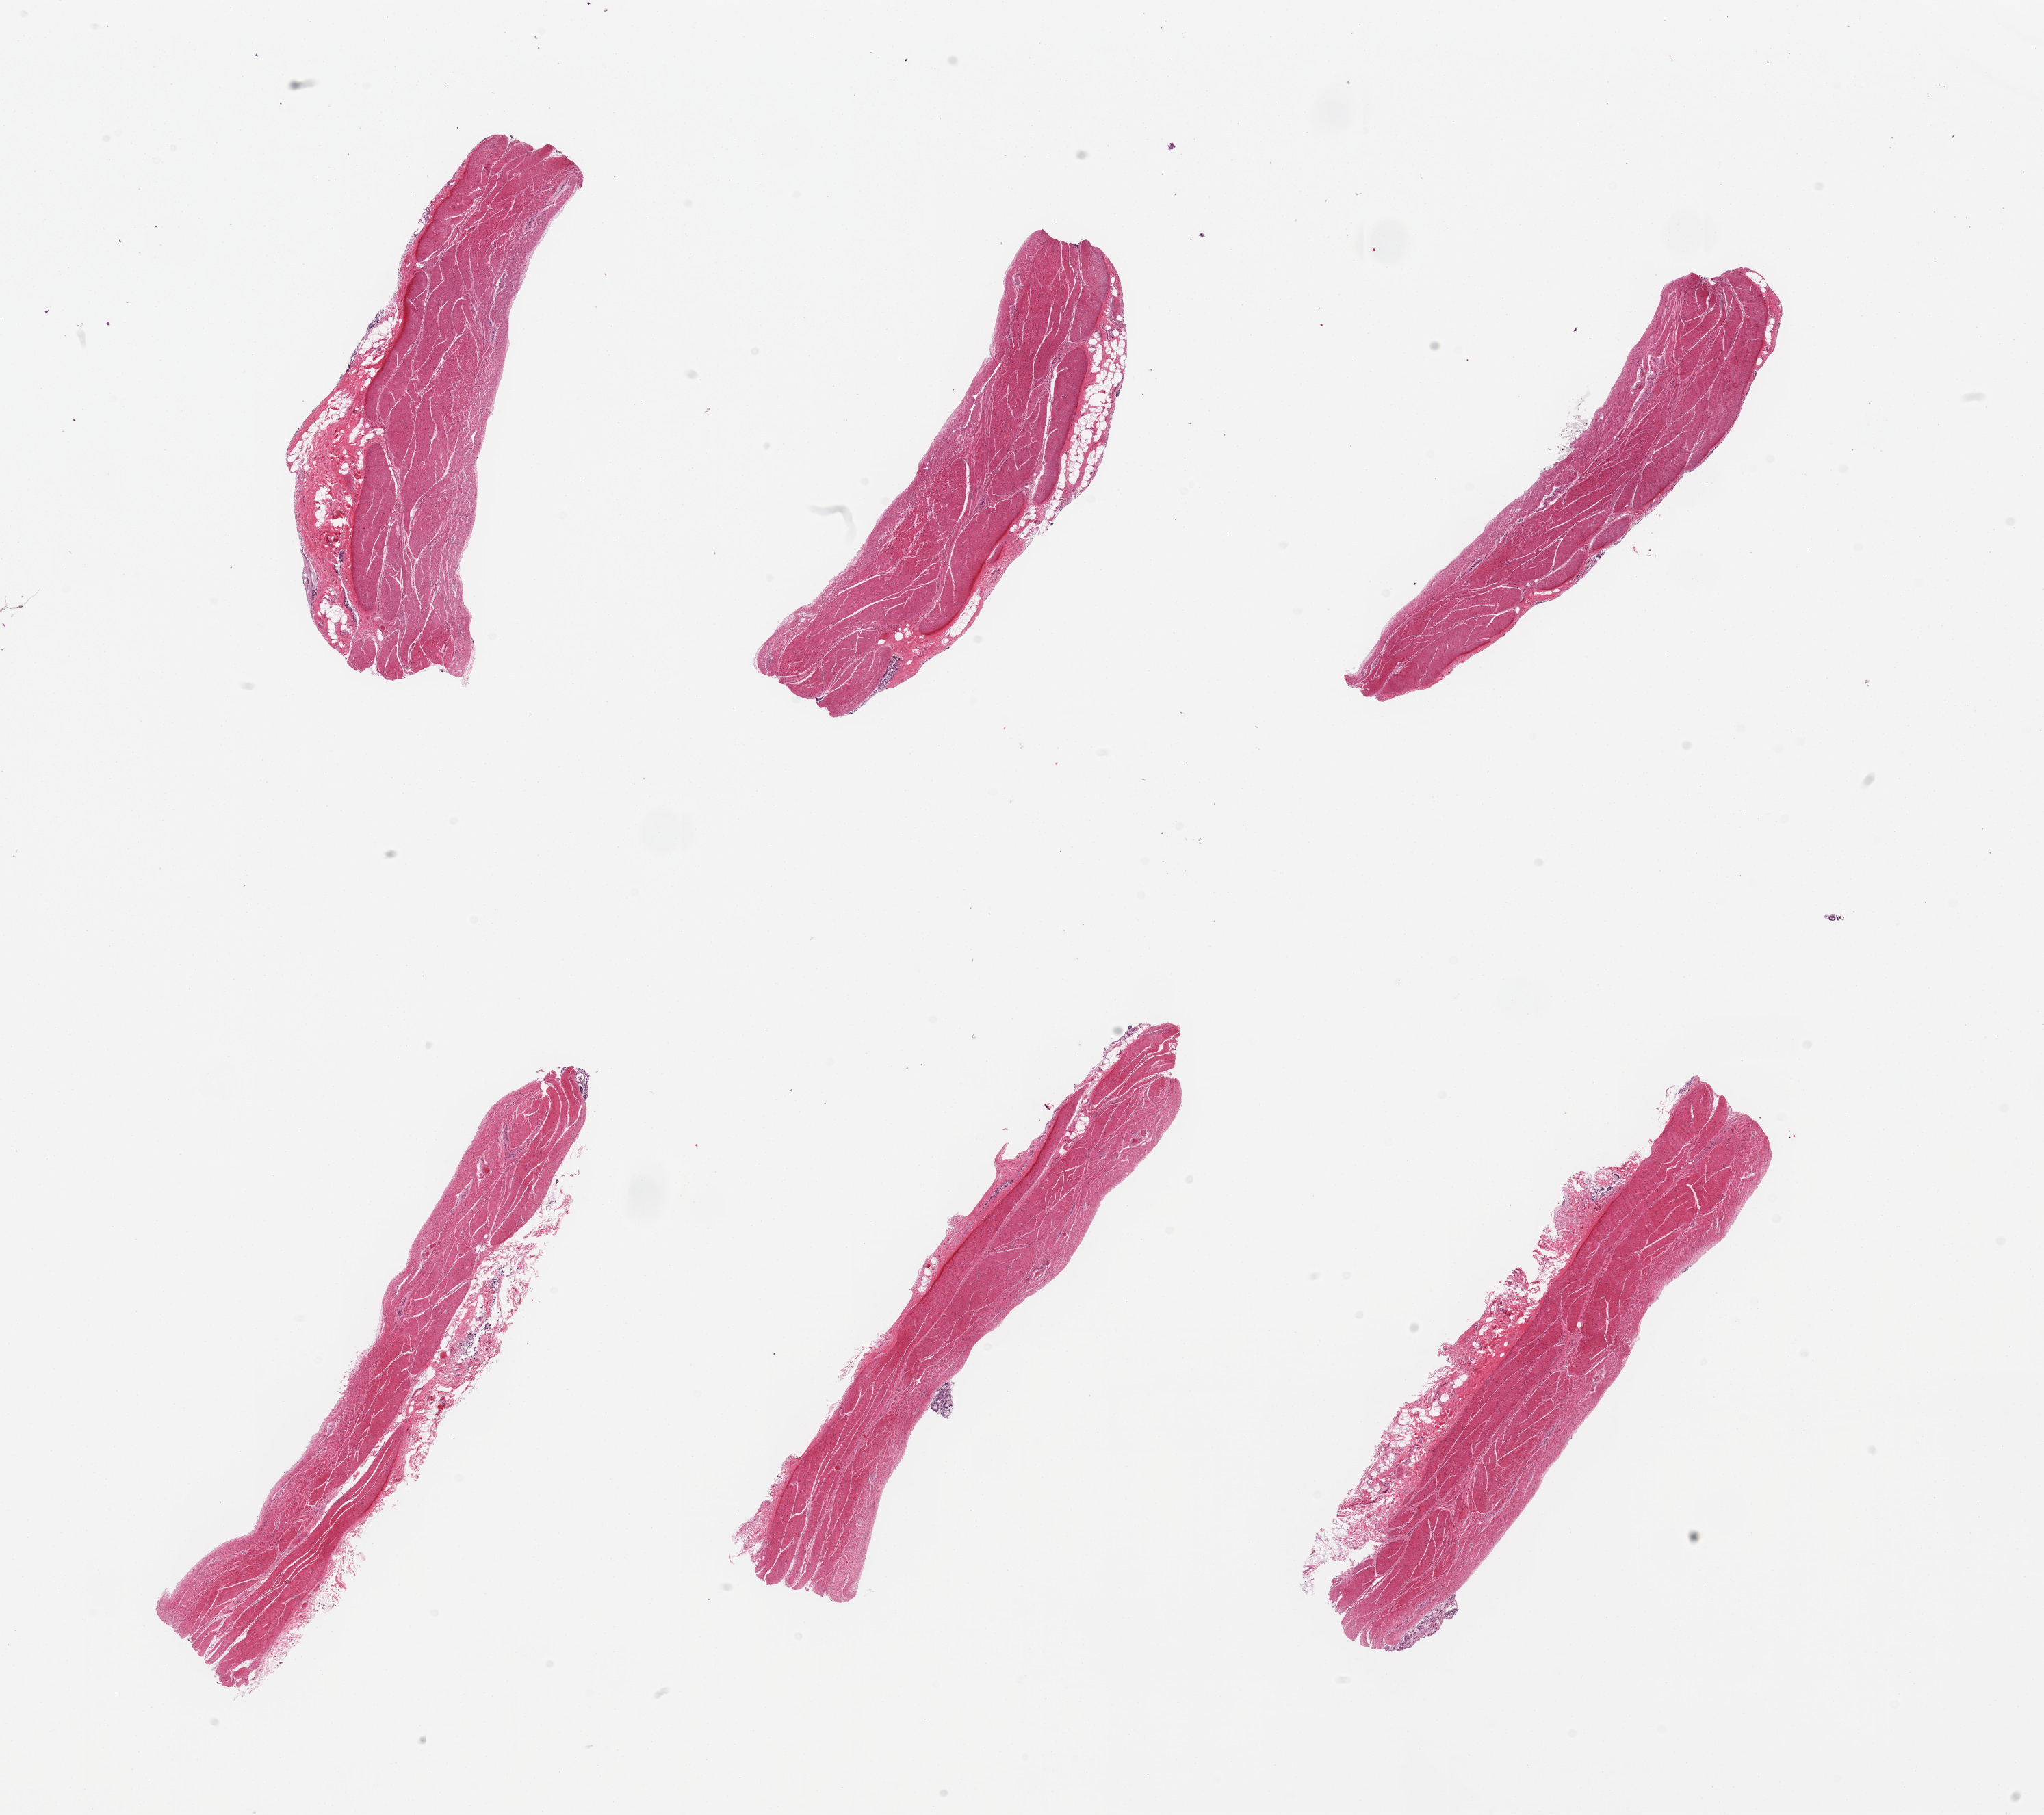
Haematoxylin and eosin whole-slide image, brightfield — whole scanned area (about 23.6 x 21.0 mm, slide scanned at 20x) shown as a low-resolution overview.
Specimen: PAXgene-fixed paraffin-embedded (PFPE) section; target tissue: stomach; donor tissue sample.